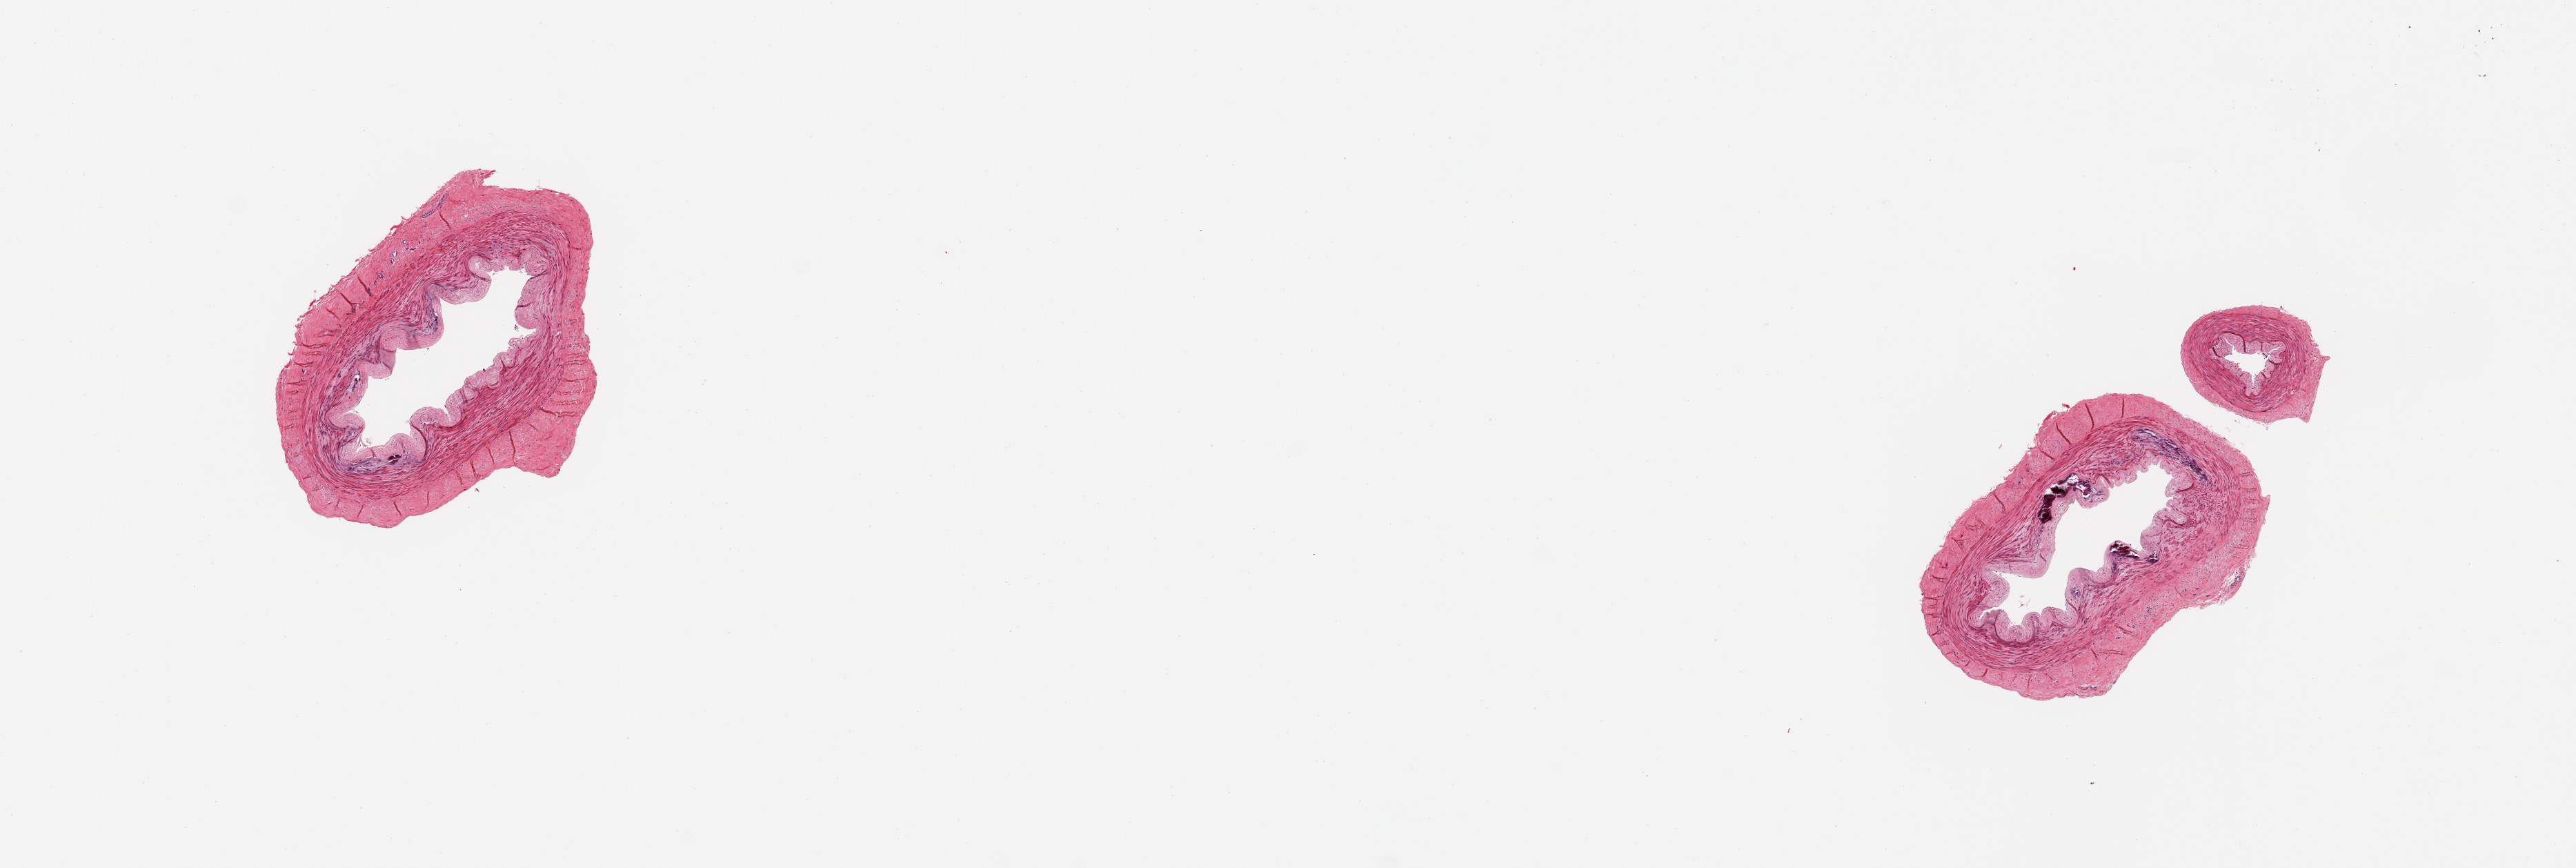
H&E whole-slide image, brightfield, shown as a low-resolution overview of the whole scanned area (about 14.8 x 5.0 mm), PAXgene-fixed paraffin-embedded (PFPE) section, target tissue: tibial artery, tissue donor sample. Donor sex: female.
Review note (as recorded): 2 pieces; foci of intimal & medial calcification; well trimmed.